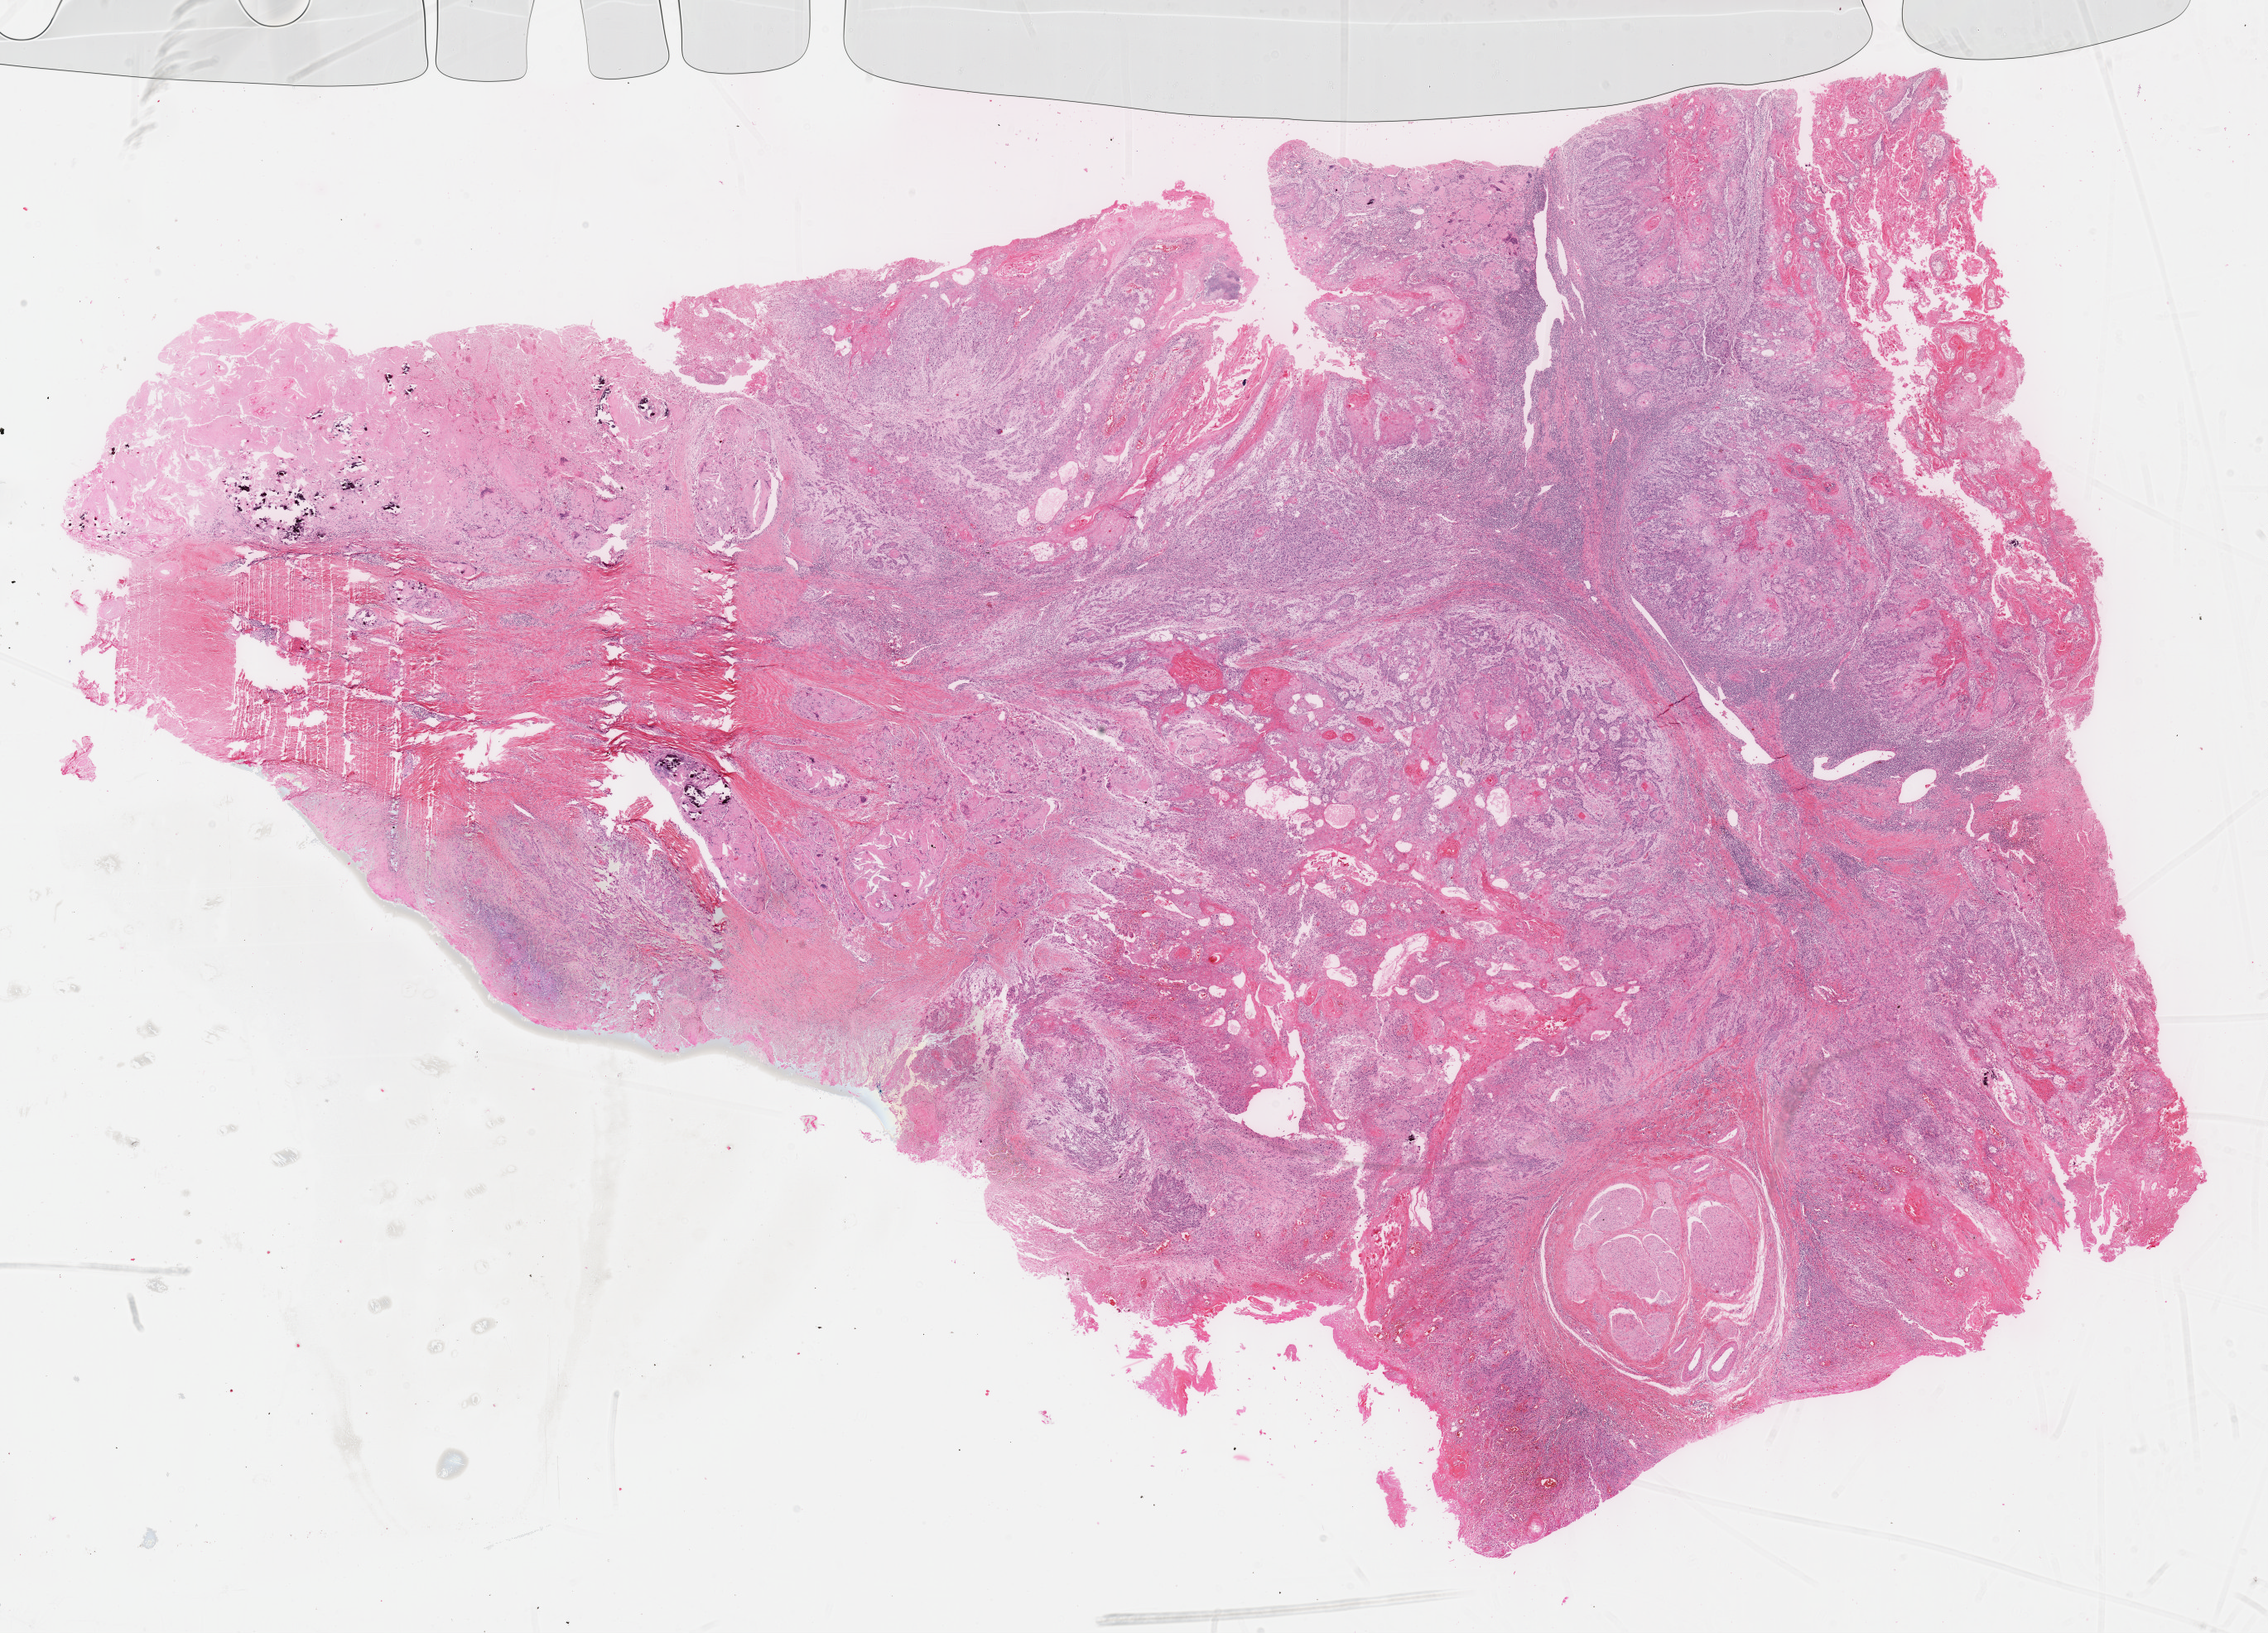
Whole-slide histology image, Hematoxylin and eosin (H&E) stained — shown as a low-resolution overview of the whole scanned area (about 22.1 x 15.9 mm, acquisition: 40x scan). Formalin-fixed paraffin-embedded (FFPE) diagnostic section. Primary tumour sample from the head and neck. Male patient; age at initial diagnosis 59 years. Histologic grade: G2 (moderately differentiated).
AJCC pathologic stage: IVA (7th edition). Lymph nodes positive (case pathology): 0 of 22 examined. Pathologic diagnosis: Squamous cell carcinoma, NOS (tongue, NOS).